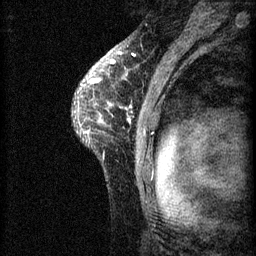
Breast MRI (dynamic contrast-enhanced), one sagittal slice; slice 49 of 60 in the series (ordered by position); 3 images stored at this slice position (order not interpretable as contrast timing); 1.5 T; TE 4.2 ms, TR 8.2 ms; 256 × 256 image matrix. Female patient, age 41 years.
Annotated regions visible in this slice (semi-automatic segmentation, software-assisted and operator-edited):
- analysis volume of interest (the breast-tissue region the enhancement analysis was run in; not a lesion): box from (x=72, y=62) to (x=159, y=175) px
- tumour enhancement mask (voxels above the 70 % enhancement threshold inside the analysis volume of interest): (x=78, y=62)–(x=131, y=135)